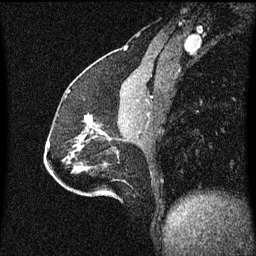
Breast MRI (dynamic contrast-enhanced), one sagittal slice; position 27 of 60 along the scan axis; dynamic contrast-enhanced series, image 2 of 3 at this slice position (ordered by acquisition); 1.5 T; TE 4.2 ms, TR 8.4 ms; 2 mm slice thickness; 256 × 256 image matrix. Female patient, age 51 years.
Structures marked on this image (semi-automatically segmented with operator editing):
- analysis volume of interest (the breast-tissue region the enhancement analysis was run in; not a lesion): box from (x=80, y=114) to (x=109, y=139) px
- tumour enhancement mask (voxels above the 70 % enhancement threshold inside the analysis volume of interest): (x=84, y=116)–(x=105, y=135)